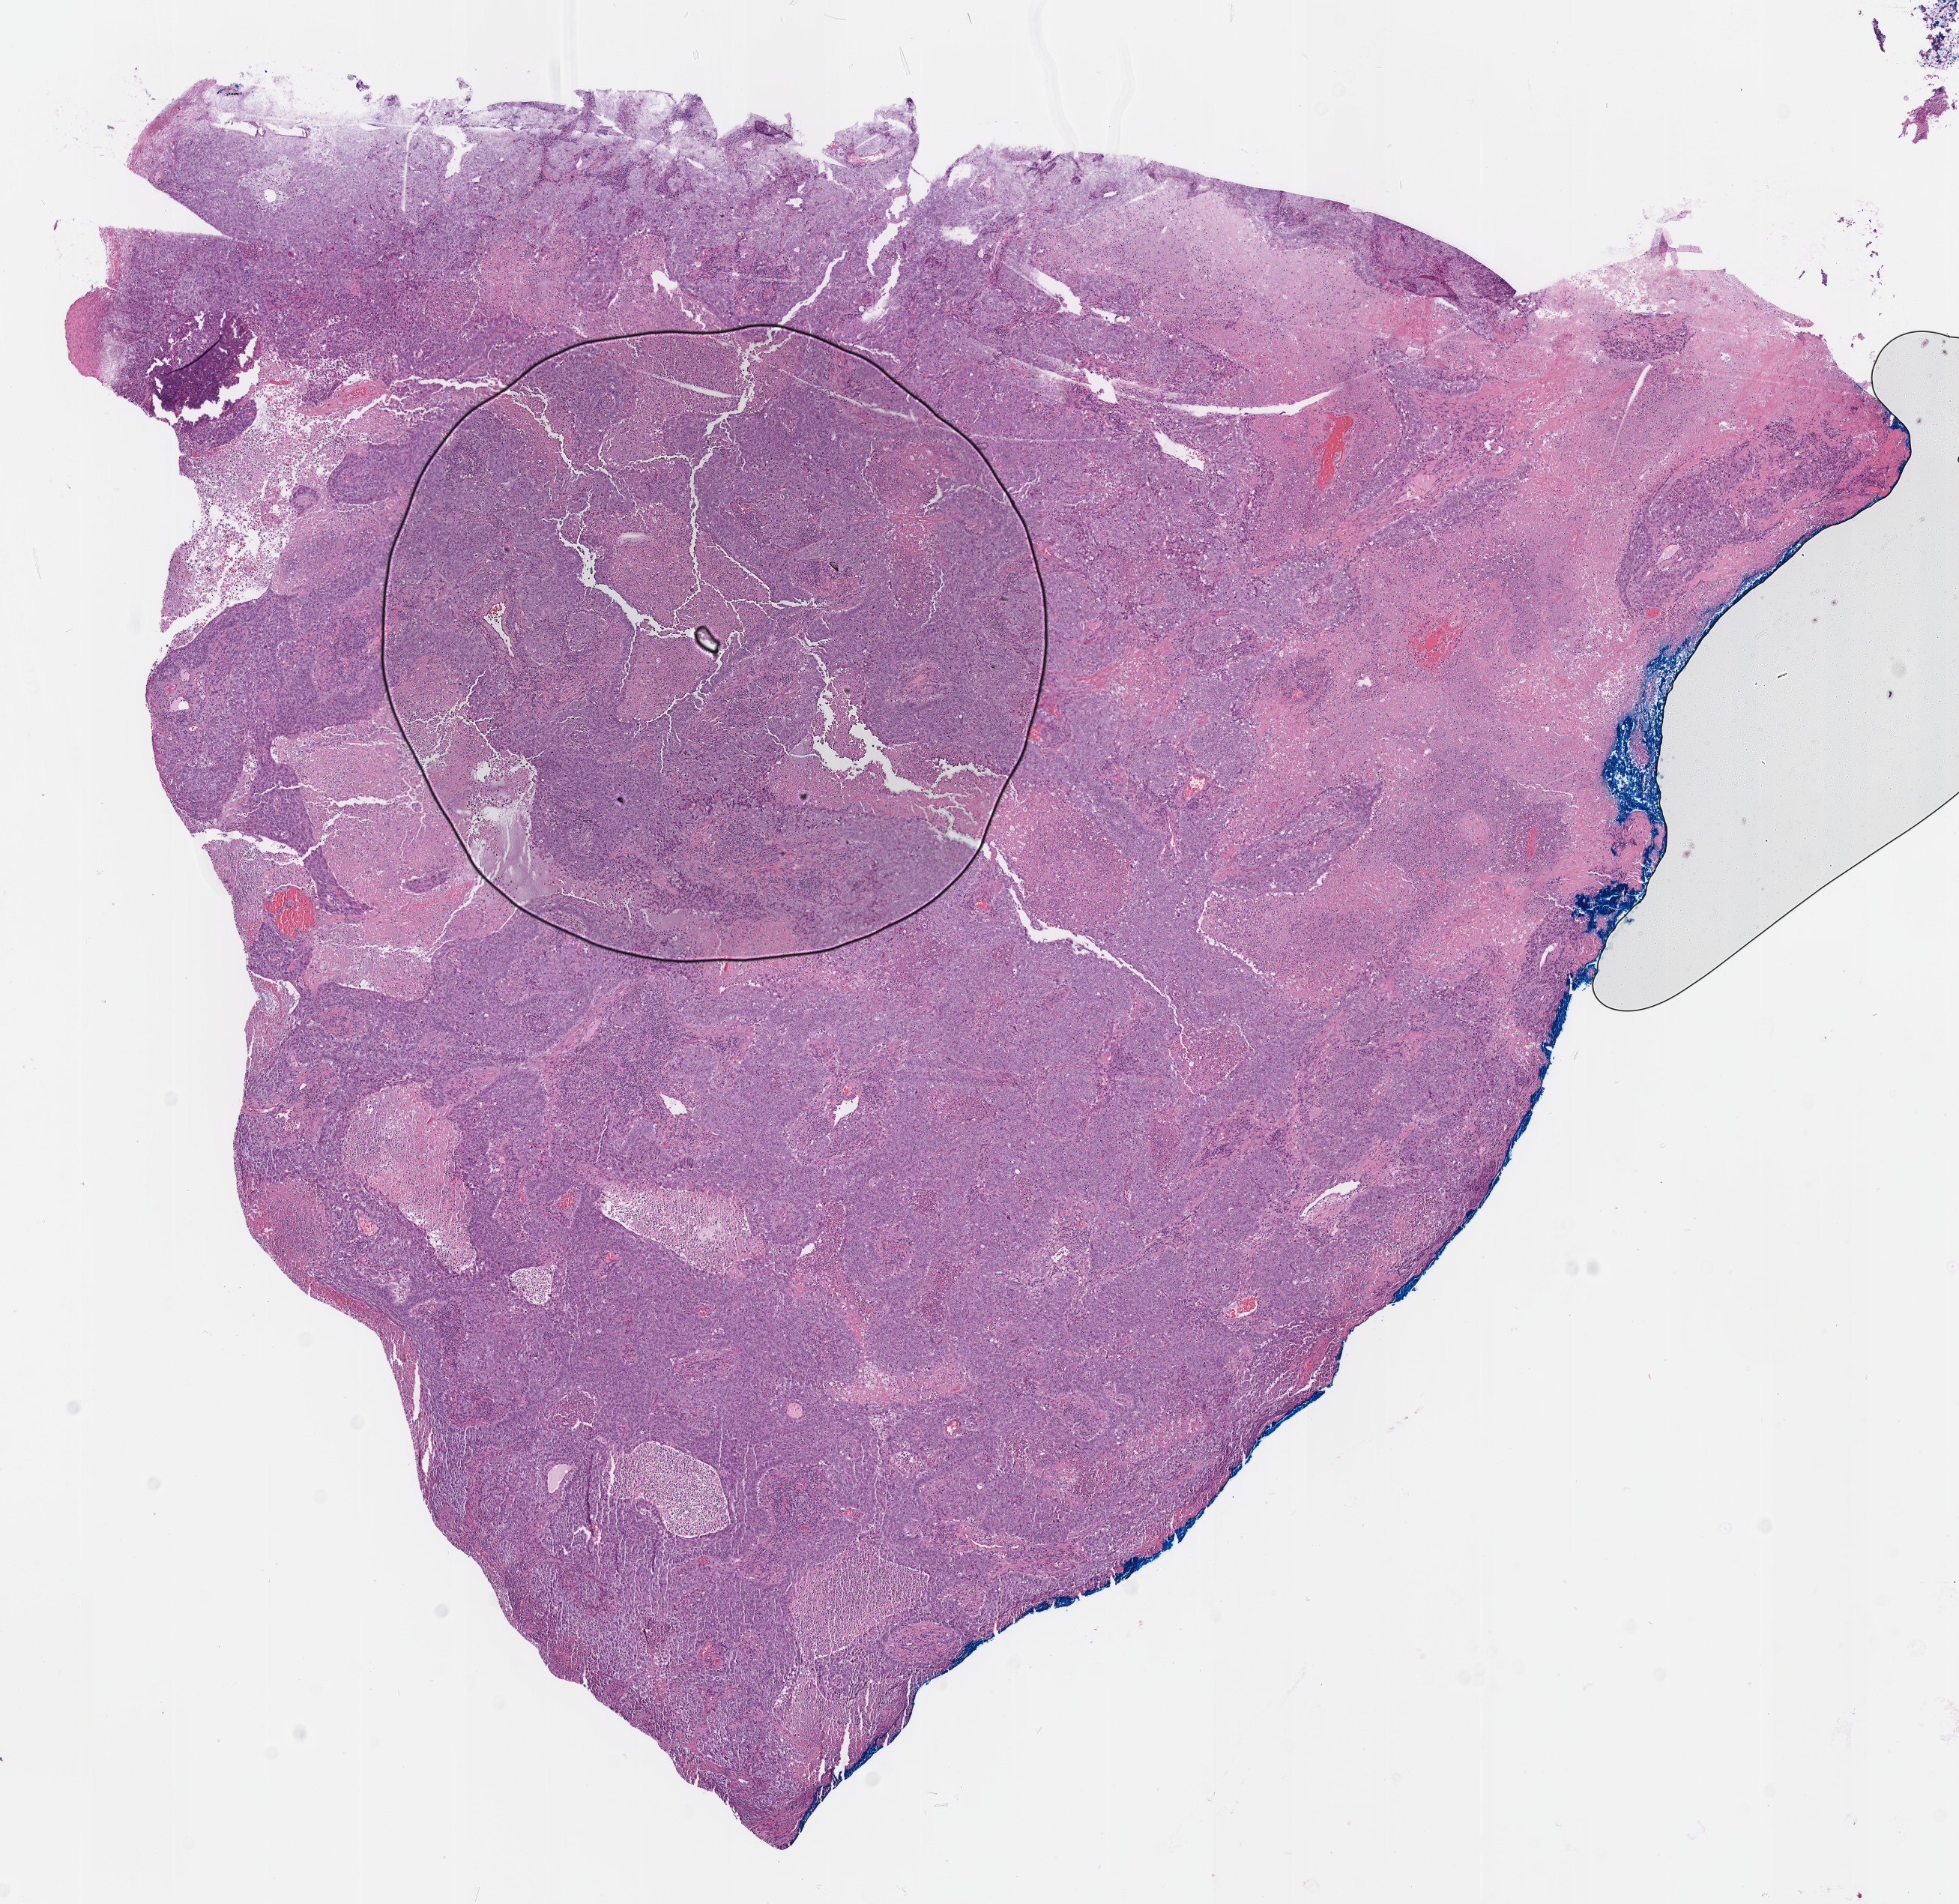
Hematoxylin and eosin (H&E) stained whole-slide image, whole scanned area (about 10.3 x 10.0 mm) shown as a low-resolution overview; FFPE section; sample: primary tumour, lung. Female, age 55 years at initial diagnosis.
Histologic diagnosis: Squamous cell carcinoma, NOS. AJCC pathologic stage: IIB (7th edition).